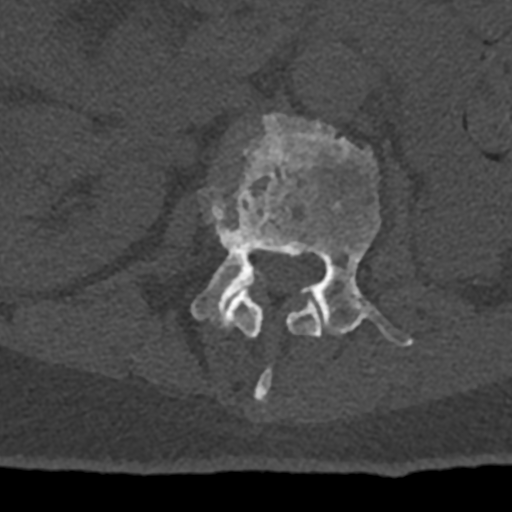
CT including the spine, one axial slice. Position 399 of 797 along the scan axis. 120 kVp. Bone window (W 1800 / L 400 HU). 0.5 mm slice thickness. 512 × 512 image matrix, field of view 160 × 160 mm. Patient: male, 74 years. From the clinical record (not read from this slice): primary cancer: renal.
Annotated regions visible in this slice (semi-automatic segmentation, software-assisted and operator-edited):
- L1 vertebra: box from (x=201, y=181) to (x=321, y=402) px
- L2 vertebra: (x=191, y=113)–(x=413, y=346)